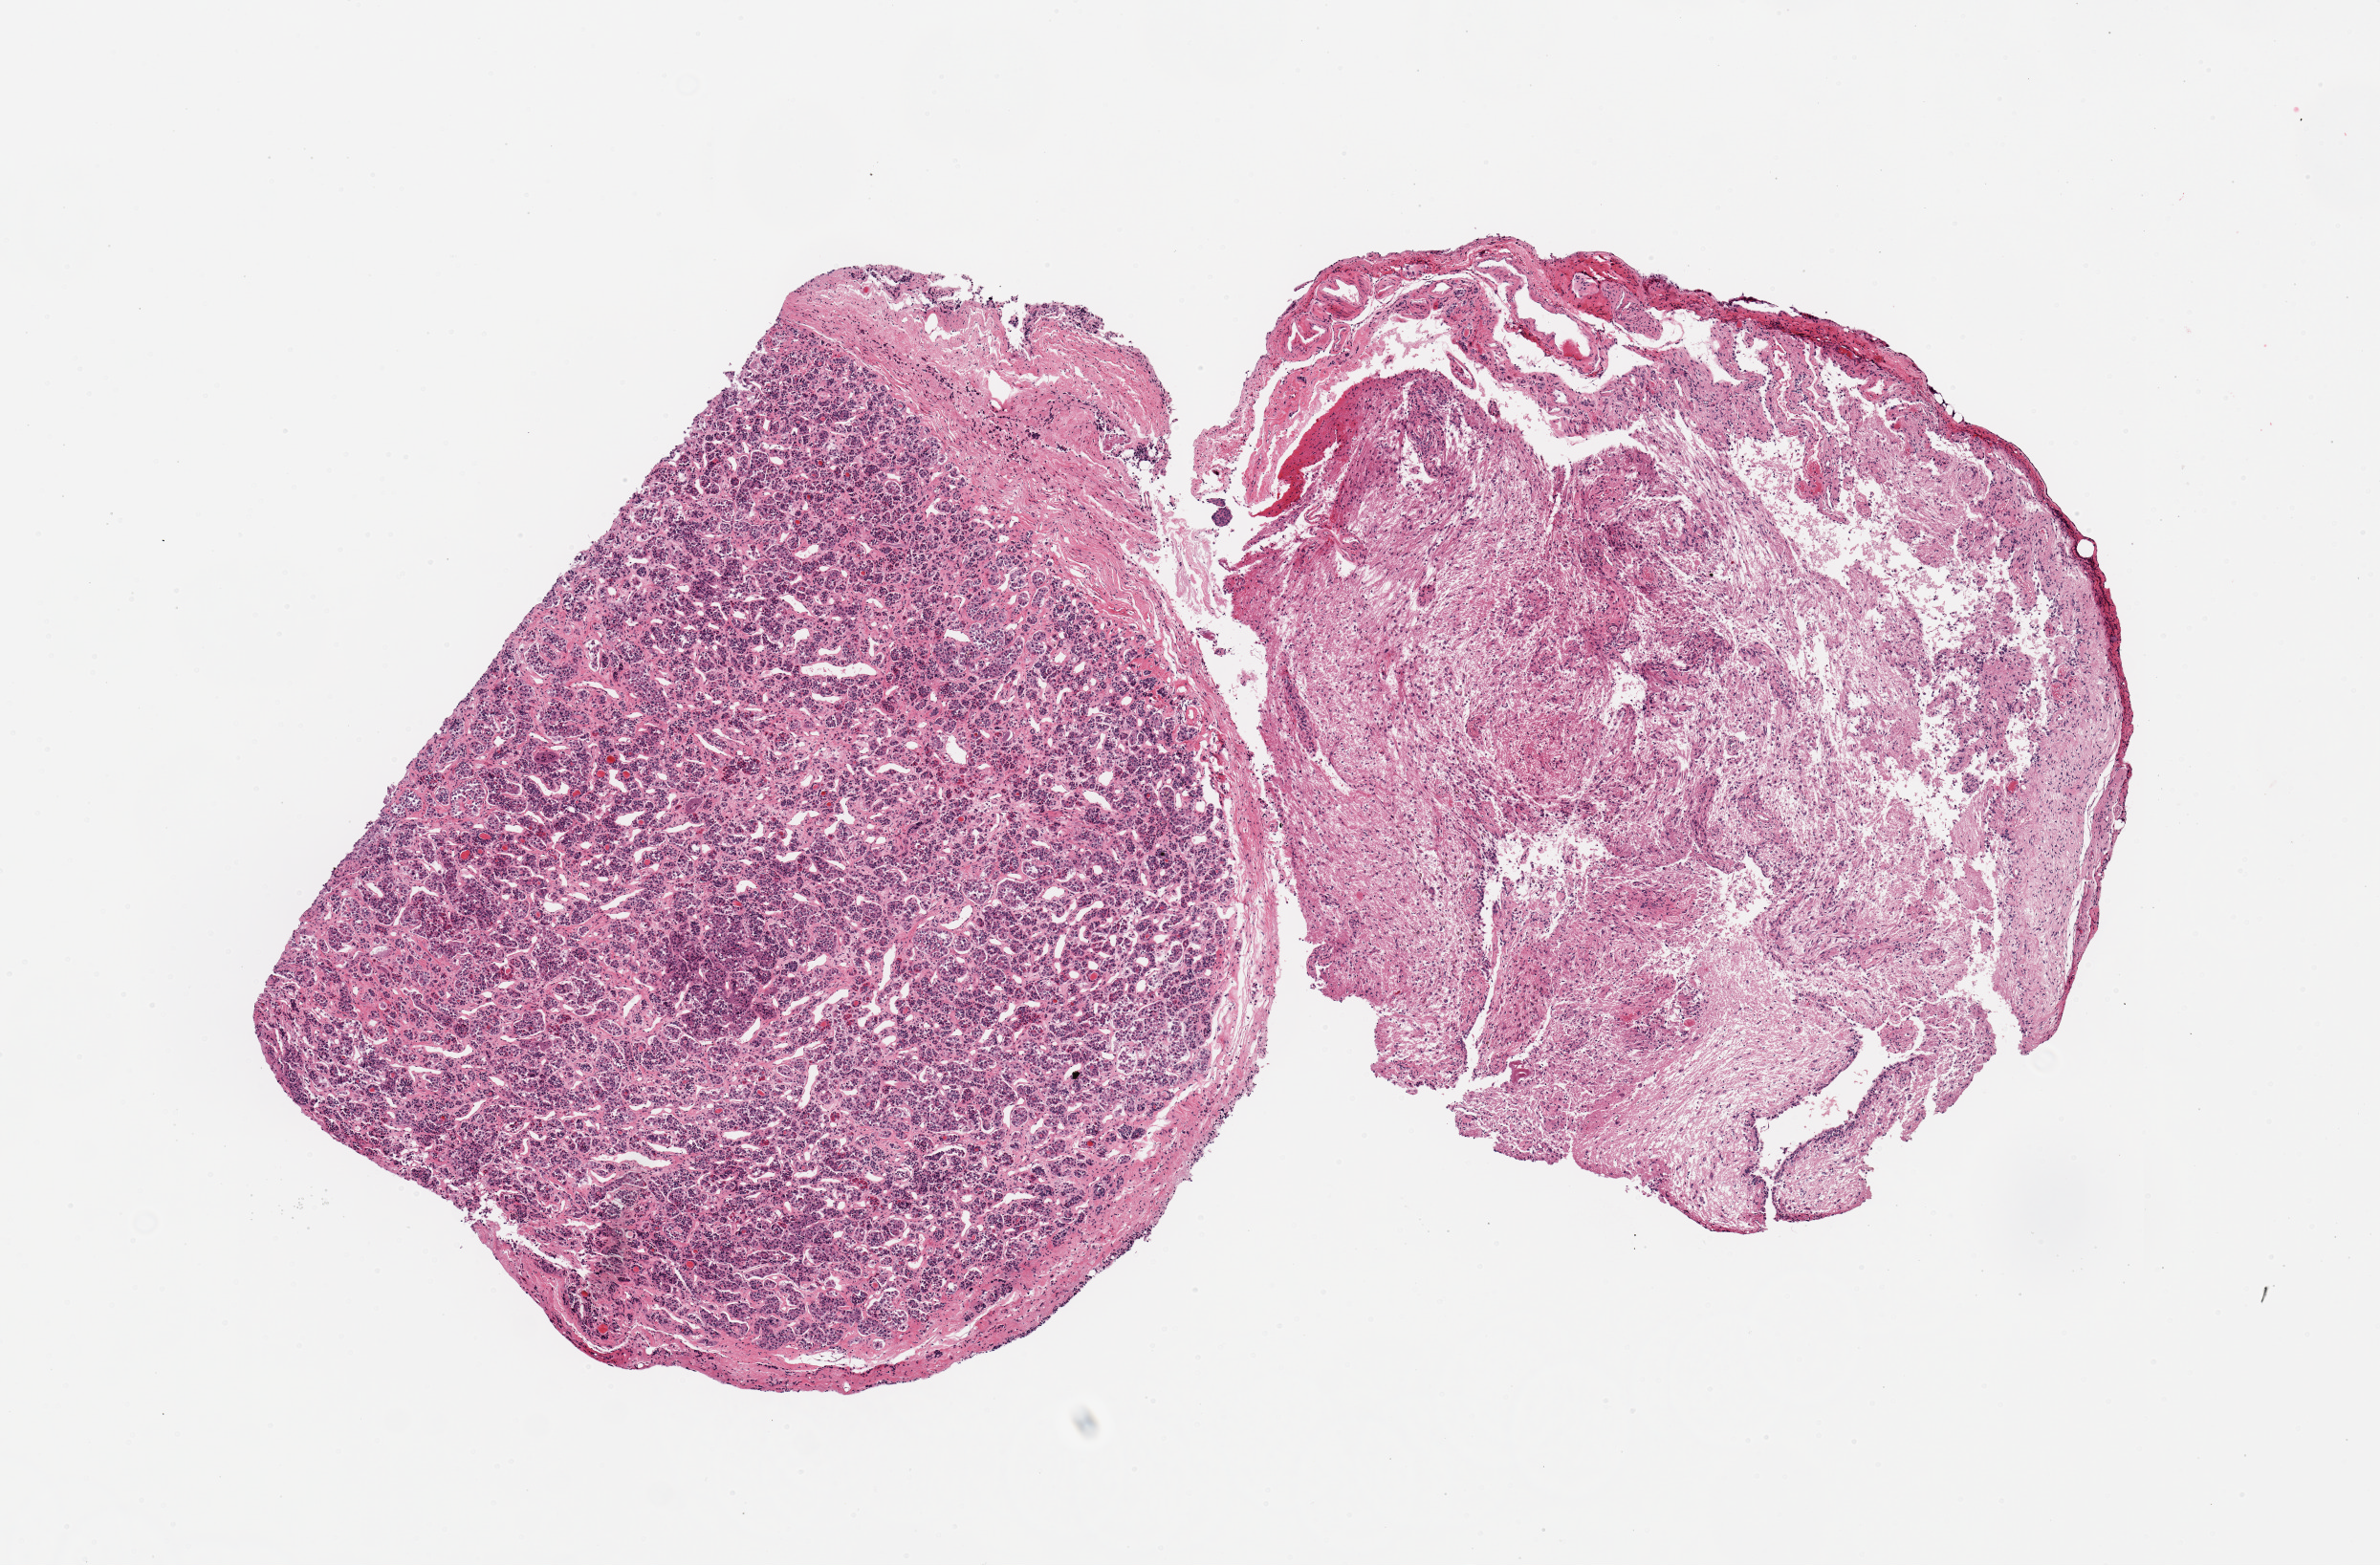
Whole-slide image, haematoxylin and eosin stain, whole scanned area (about 9.8 x 6.5 mm, acquisition: 20x scan) shown as a low-resolution overview; PAXgene-fixed paraffin-embedded (PFPE) section; sampled site (target tissue): pituitary; tissue donor sample. Donor sex: male.
Reviewer comment on this tissue sample: 2 pieces; anterior and posterior parts are separated and in equal proportions.